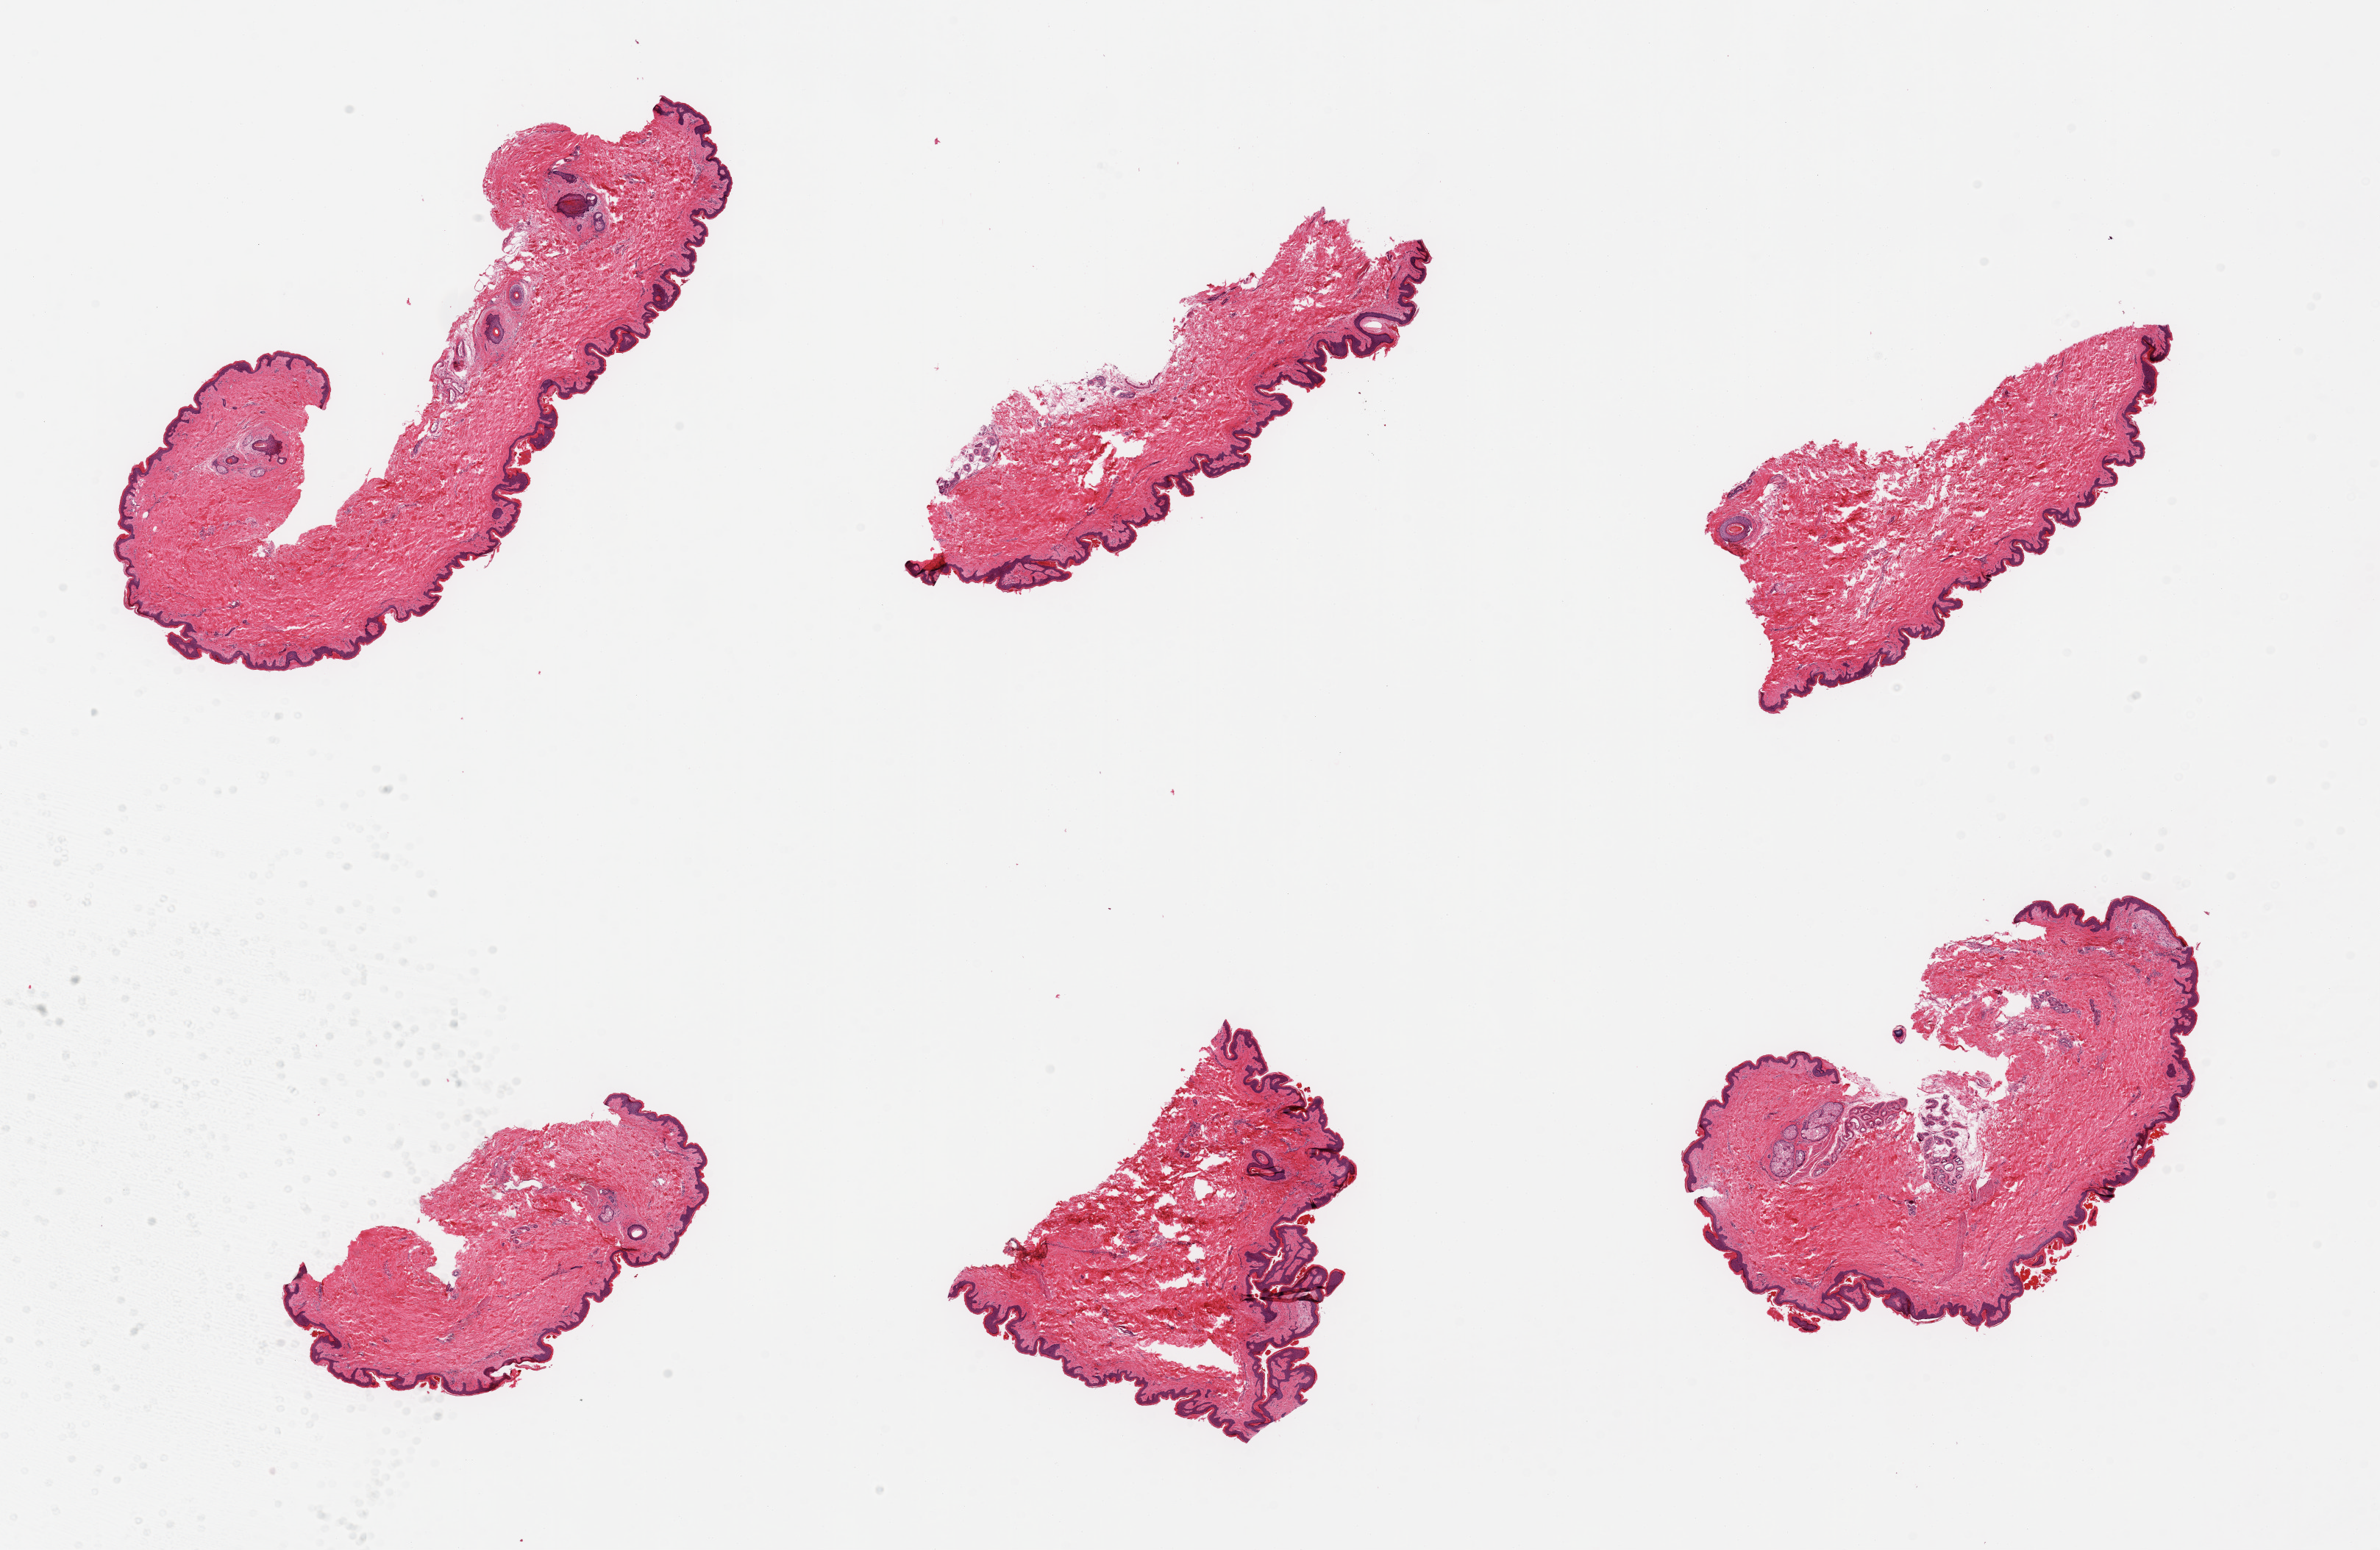
Digitized H&E-stained section, brightfield, a low-resolution overview of the entire scanned area, about 25.6 x 16.7 mm (slide scanned at 20x), PAXgene-fixed paraffin-embedded (PFPE) section, sampled site (target tissue): skin of suprapubic region, tissue donor sample. Donor sex: male.
- pathologist's review note for this sample: 6 pieces, no dermal fat; squamous epithelium is ~30-40 microns